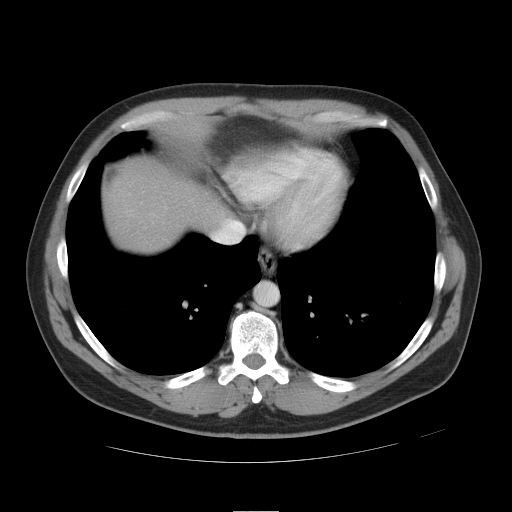
Contrast-enhanced abdominal CT, one axial slice; position 43 of 49 along the scan axis; reconstruction kernel STANDARD; 120 kVp; soft-tissue window (W 400 / L 40 HU); 5 mm slice thickness; 512 × 512 image matrix, field of view 425 × 425 mm. Male patient, age 52 years. Case-level facts recorded for this patient, not image findings: diagnosis: colorectal cancer liver metastases, imaged before liver resection; multiple liver metastases: yes; largest metastasis: 5.1 cm.
Outlined on this slice (manually delineated by an expert):
- liver: bounding box (x1, y1, x2, y2) in pixels: (106, 168, 224, 252)
- planned liver remnant (the part of the liver to remain after resection): (172, 183, 224, 223)